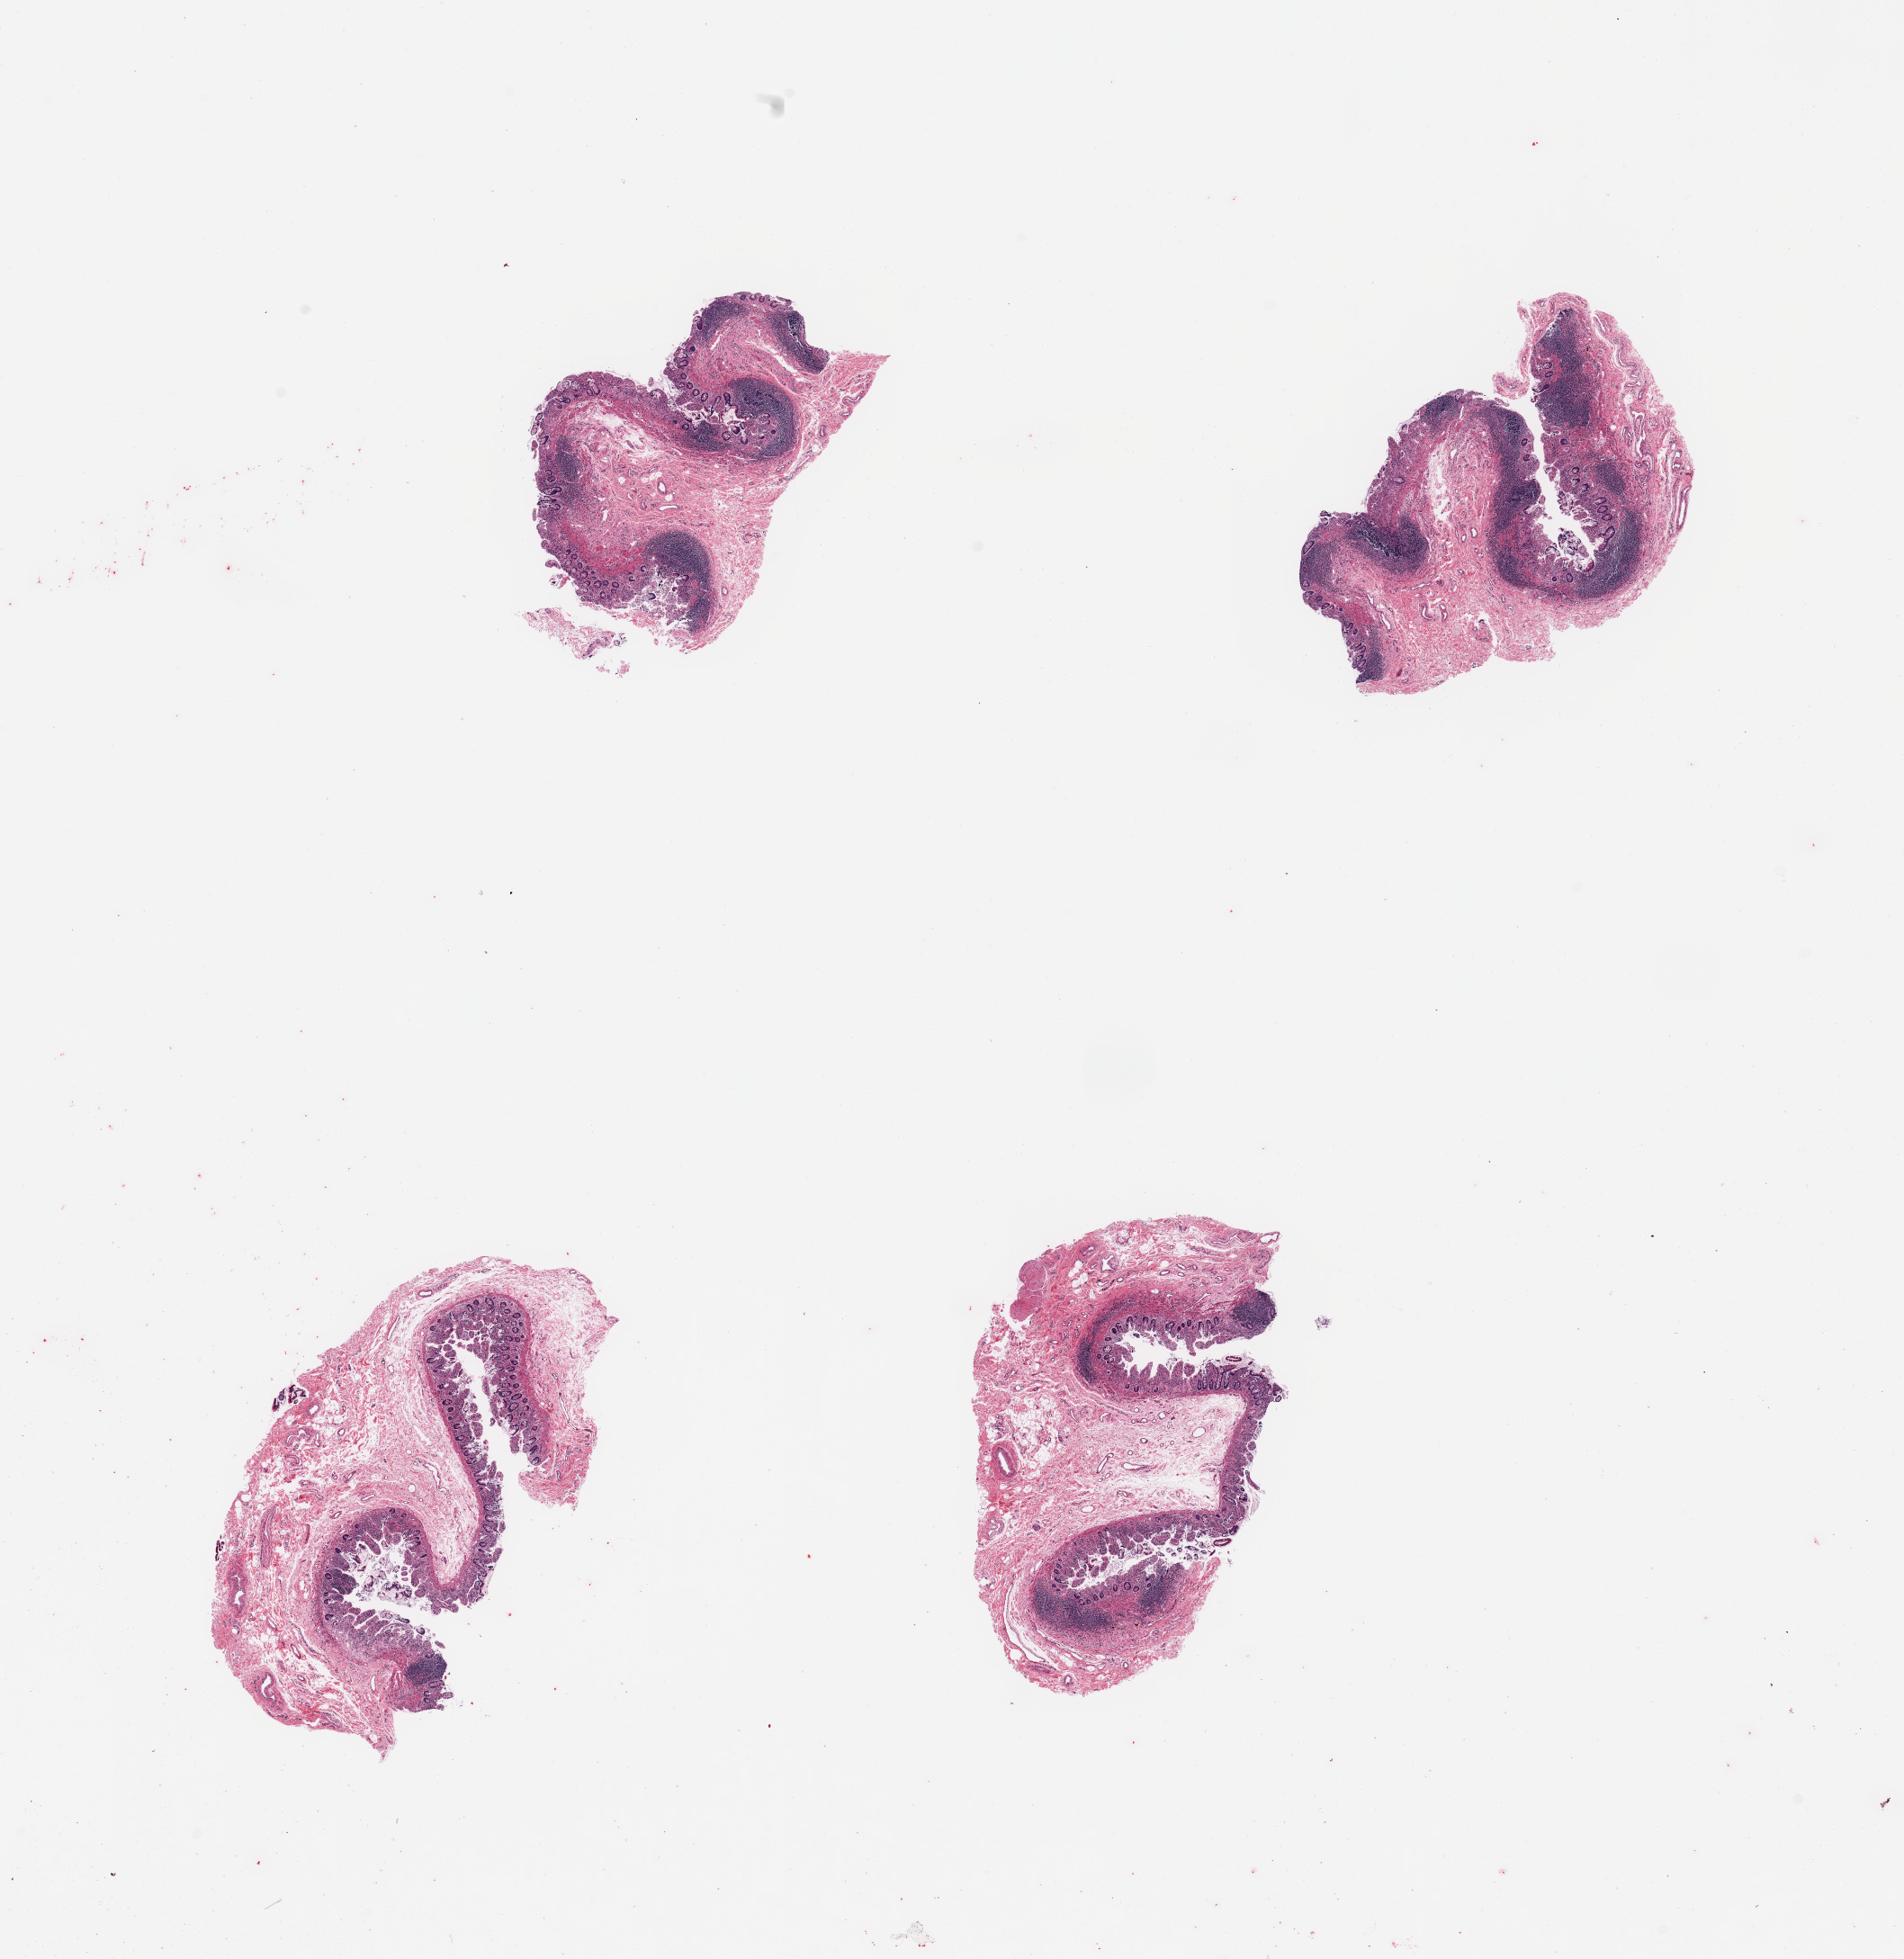
Whole-slide image, H&E stain, brightfield, whole scanned area (about 16.7 x 17.2 mm) shown as a low-resolution overview, PAXgene-fixed, paraffin-embedded tissue, section of ileum (target tissue), tissue donor sample. Donor: male.
- pathologist's review note for this sample: 4 pieces, ~5-10% target lymphoid aggregates